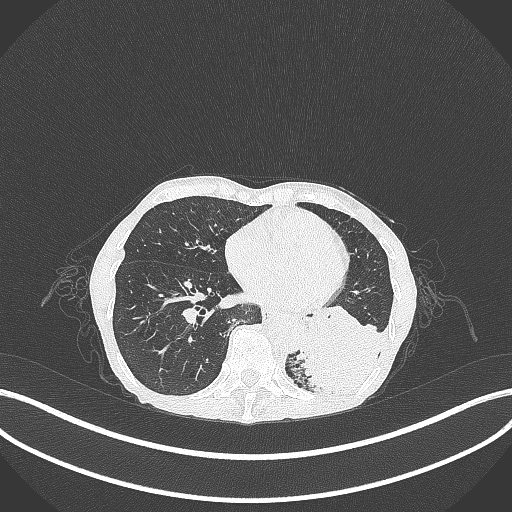
Chest CT, one axial slice. Position 91 of 347 along the scan axis. Reconstruction kernel B70f. Lung window (W 1500 / L -600 HU). 1 mm slice thickness. 512 × 512 image matrix, field of view 400 × 400 mm. Patient: female, 70 years. From the clinical record (not read from this slice): clinical TNM (as recorded): T3 N0 M0; histopathological grade: G3.
Structures marked on this image (bounding box drawn by a radiologist):
- lung tumour (recorded histology: small cell carcinoma): bounding box [x1, y1, x2, y2] px = [298, 313, 394, 403]